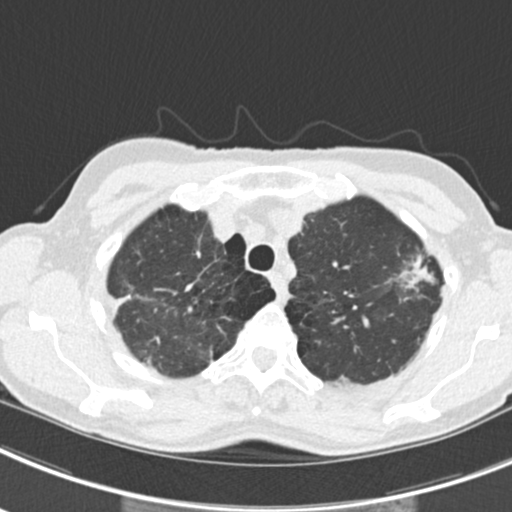
Axial slice from a low-dose chest CT screening exam, second annual screen, lung window (W 1500 / L -600 HU), 2 mm slice thickness, 120 kVp, 512 × 512 image matrix. Female, age 63 years at enrolment. Current smoker at enrolment.
Lesion marked by an expert reader, bounding box <380,243,445,305> (left, top, right, bottom; pixels). The screening reader recorded 9 non-calcified nodules or masses ≥4 mm on this exam; which of them this box marks is not recorded. Lung cancer was diagnosed 408 days after this screen (after the third annual screen): bronchiolo-alveolar adenocarcinoma, NOS, right upper lobe, right middle lobe, right lower lobe, left upper lobe, left lower lobe, moderately differentiated (G2), stage IV (AJCC 6th edition).